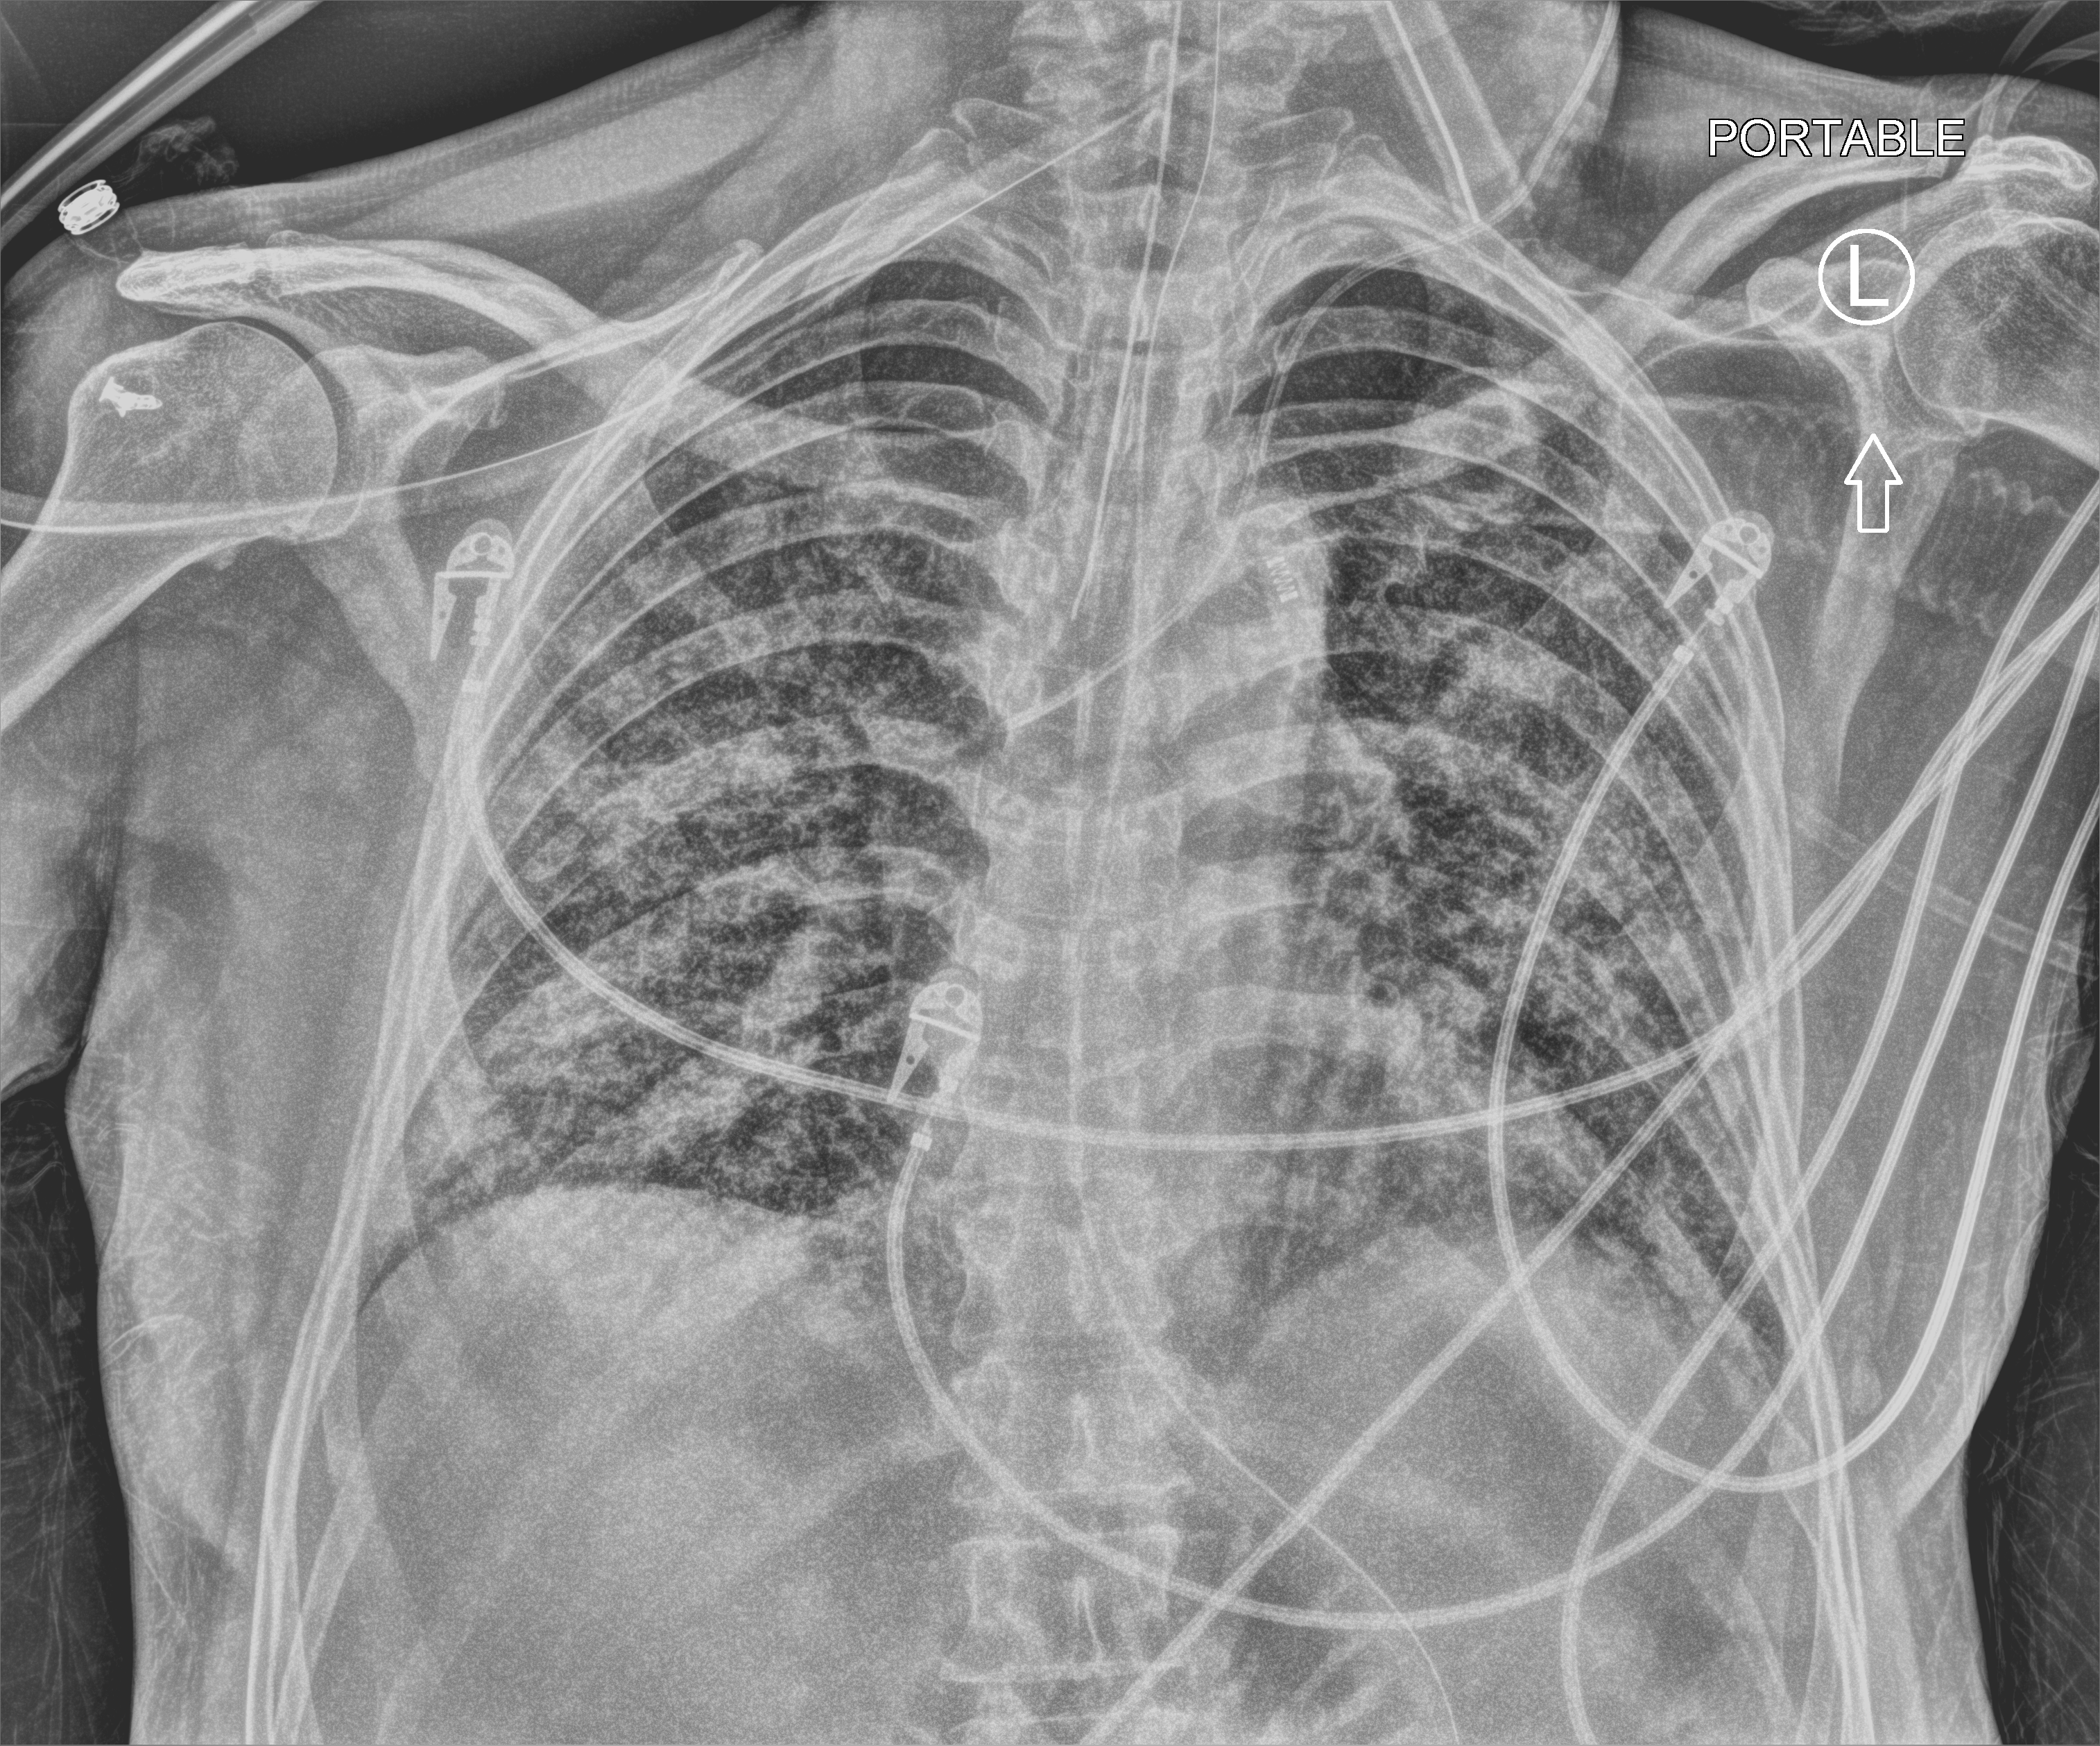
Portable chest radiograph; anteroposterior (AP) projection. Patient hospitalised with COVID-19; male, aged 60–74 years.
Admission-level facts for this patient (not findings on this image; timing relative to this image not recorded): hypertension (admission record): no; admitted to intensive care during this hospital stay: yes.